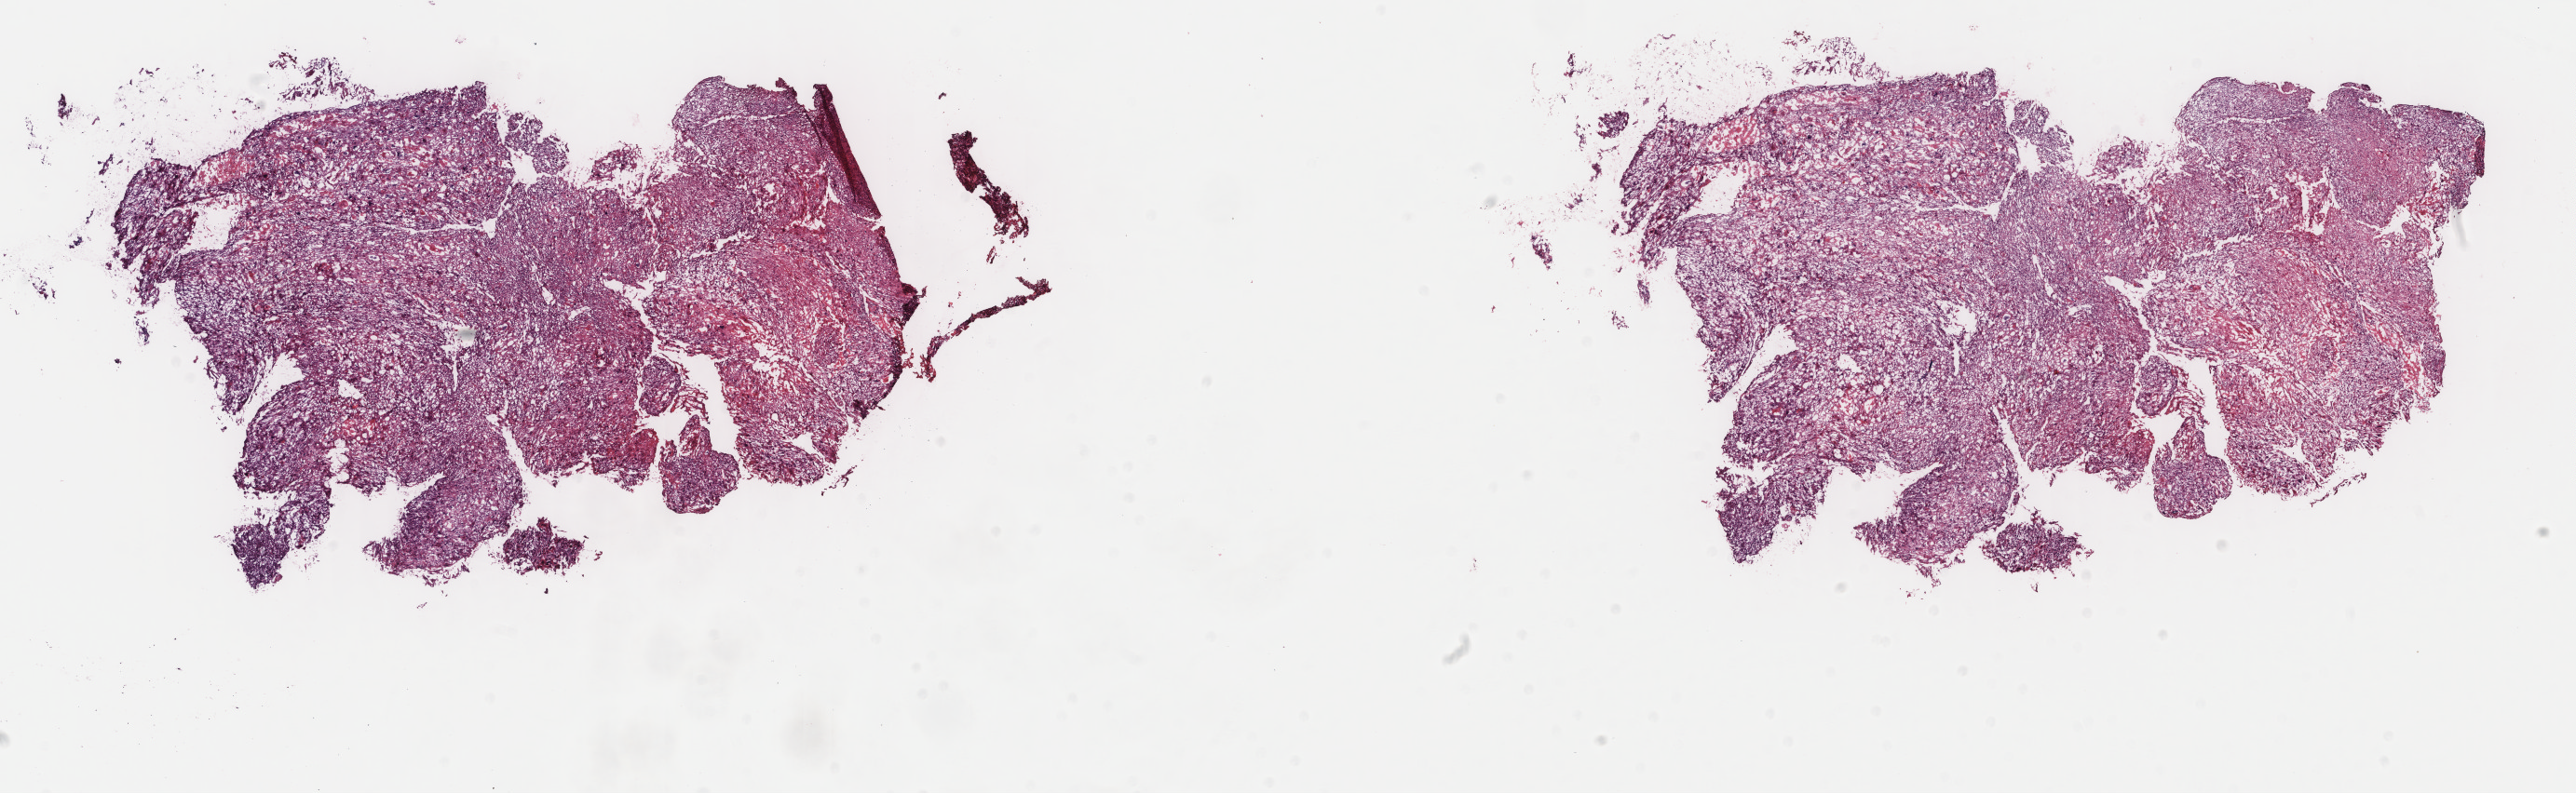
Hematoxylin and eosin (H&E) stained whole-slide image, a low-resolution overview of the entire scanned area, about 22.0 x 6.8 mm (from a 40x scan). Frozen section from the top of the tissue portion. Sample: primary tumour, cervix. Female patient; age at initial diagnosis 45 years. Pathologist review of this section (percent, as recorded): tumour cells 95%, tumour nuclei 98%.
Diagnosis: Squamous cell carcinoma, keratinizing, NOS.